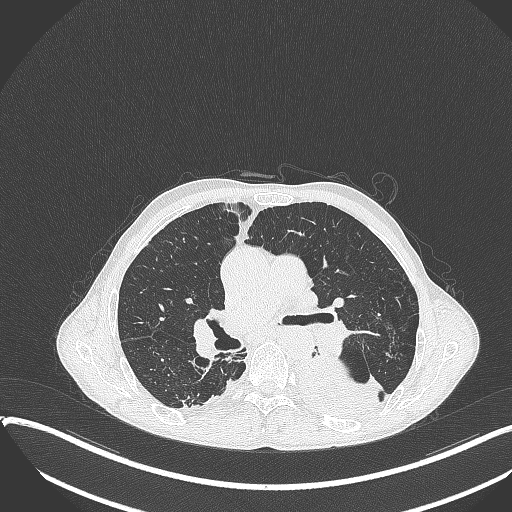
Chest CT, one axial slice; slice 223 of 401 in the series (ordered by position); 120 kVp; lung window (W 1500 / L -600 HU); 512 × 512 image matrix, field of view 400 × 400 mm. Patient: male, 57 years. Case-level facts recorded for this patient, not image findings: clinical TNM (as recorded): T4 N0 M0.
Outlined on this slice (rectangle marked by the reading radiologist):
- lung tumour (recorded histology: squamous cell carcinoma): bounding box <291,353,383,421> (left, top, right, bottom; pixels)